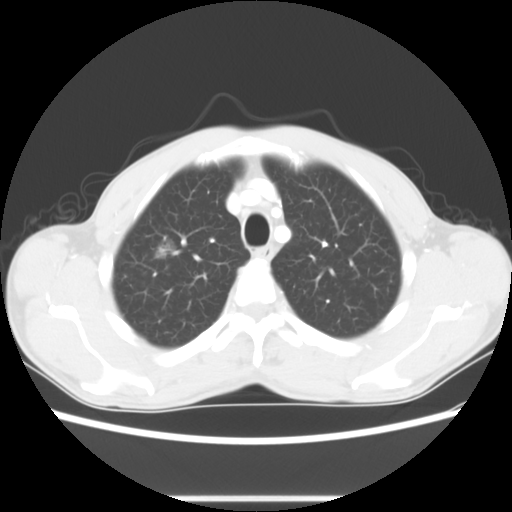
Chest CT, one axial slice. Slice 58 of 73 in the series (ordered by position). Lung window (W 1500 / L -600 HU). 5 mm slice thickness. 512 × 512 image matrix. Male patient, age 54 years. Case-level facts recorded for this patient, not image findings: clinical TNM (as recorded): T1a N0 M0.
Structures marked on this image (bounding box drawn by a radiologist):
- lung tumour (recorded histology: adenocarcinoma): box from (x=146, y=230) to (x=181, y=267) px